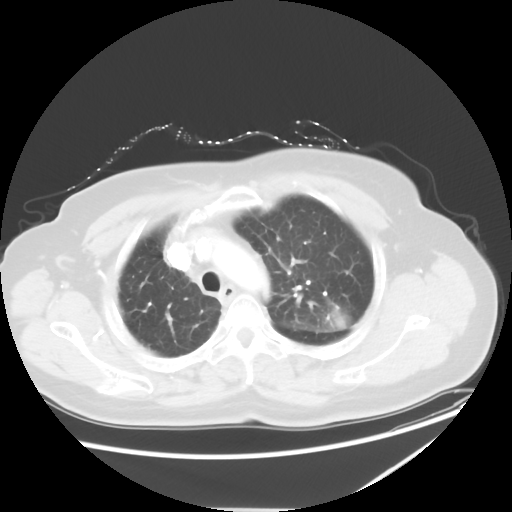
Chest CT, one axial slice; position 42 of 54 along the scan axis; reconstruction kernel STANDARD; 120 kVp; lung window (W 1500 / L -600 HU); 5 mm slice thickness; 512 × 512 image matrix, field of view 384 × 384 mm. Patient: female, 61 years. Case-level facts recorded for this patient, not image findings: clinical TNM (as recorded): T1c N3 M1.
Outlined on this slice (rectangle marked by the reading radiologist):
- lung tumour (recorded histology: adenocarcinoma): bounding box (x1, y1, x2, y2) in pixels: (316, 290, 356, 339)